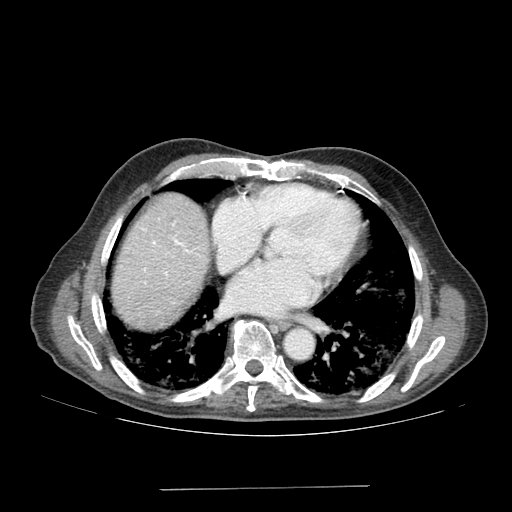
Contrast-enhanced abdominal CT (liver protocol), one axial slice; position 172 of 192 along the scan axis; reconstruction kernel SOFT; 120 kVp; soft-tissue window (W 400 / L 40 HU); 2.5 mm slice thickness; 512 × 512 image matrix. Case-level facts recorded for this patient, not image findings: diagnosis: hepatocellular carcinoma (patient treated with transarterial chemoembolisation; whether this scan precedes or follows treatment is not stated here); TNM stage (as recorded): Stage-IVA; Child-Pugh class: A; tumour differentiation: poorly differentiated.
Annotated regions visible in this slice (semi-automatic segmentation, software-assisted and operator-edited):
- liver parenchyma outside the tumour (the mass and vessels are separate outlines, so this box may not span the whole liver): bounding box (x1, y1, x2, y2) in pixels: (112, 194, 209, 326)
- liver vessels: (144, 223, 189, 275)